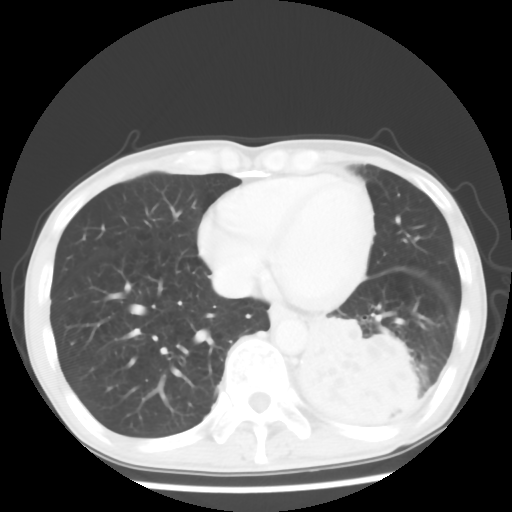
Chest CT, one axial slice; 120 kVp; lung window (W 1500 / L -600 HU); 512 × 512 image matrix, field of view 313 × 313 mm. Male patient, age 68 years. Case-level facts recorded for this patient, not image findings: clinical TNM (as recorded): T4 N0 M0.
Outlined on this slice (rectangle marked by the reading radiologist):
- lung tumour (recorded histology: squamous cell carcinoma): bounding box <285,306,428,438> (left, top, right, bottom; pixels)